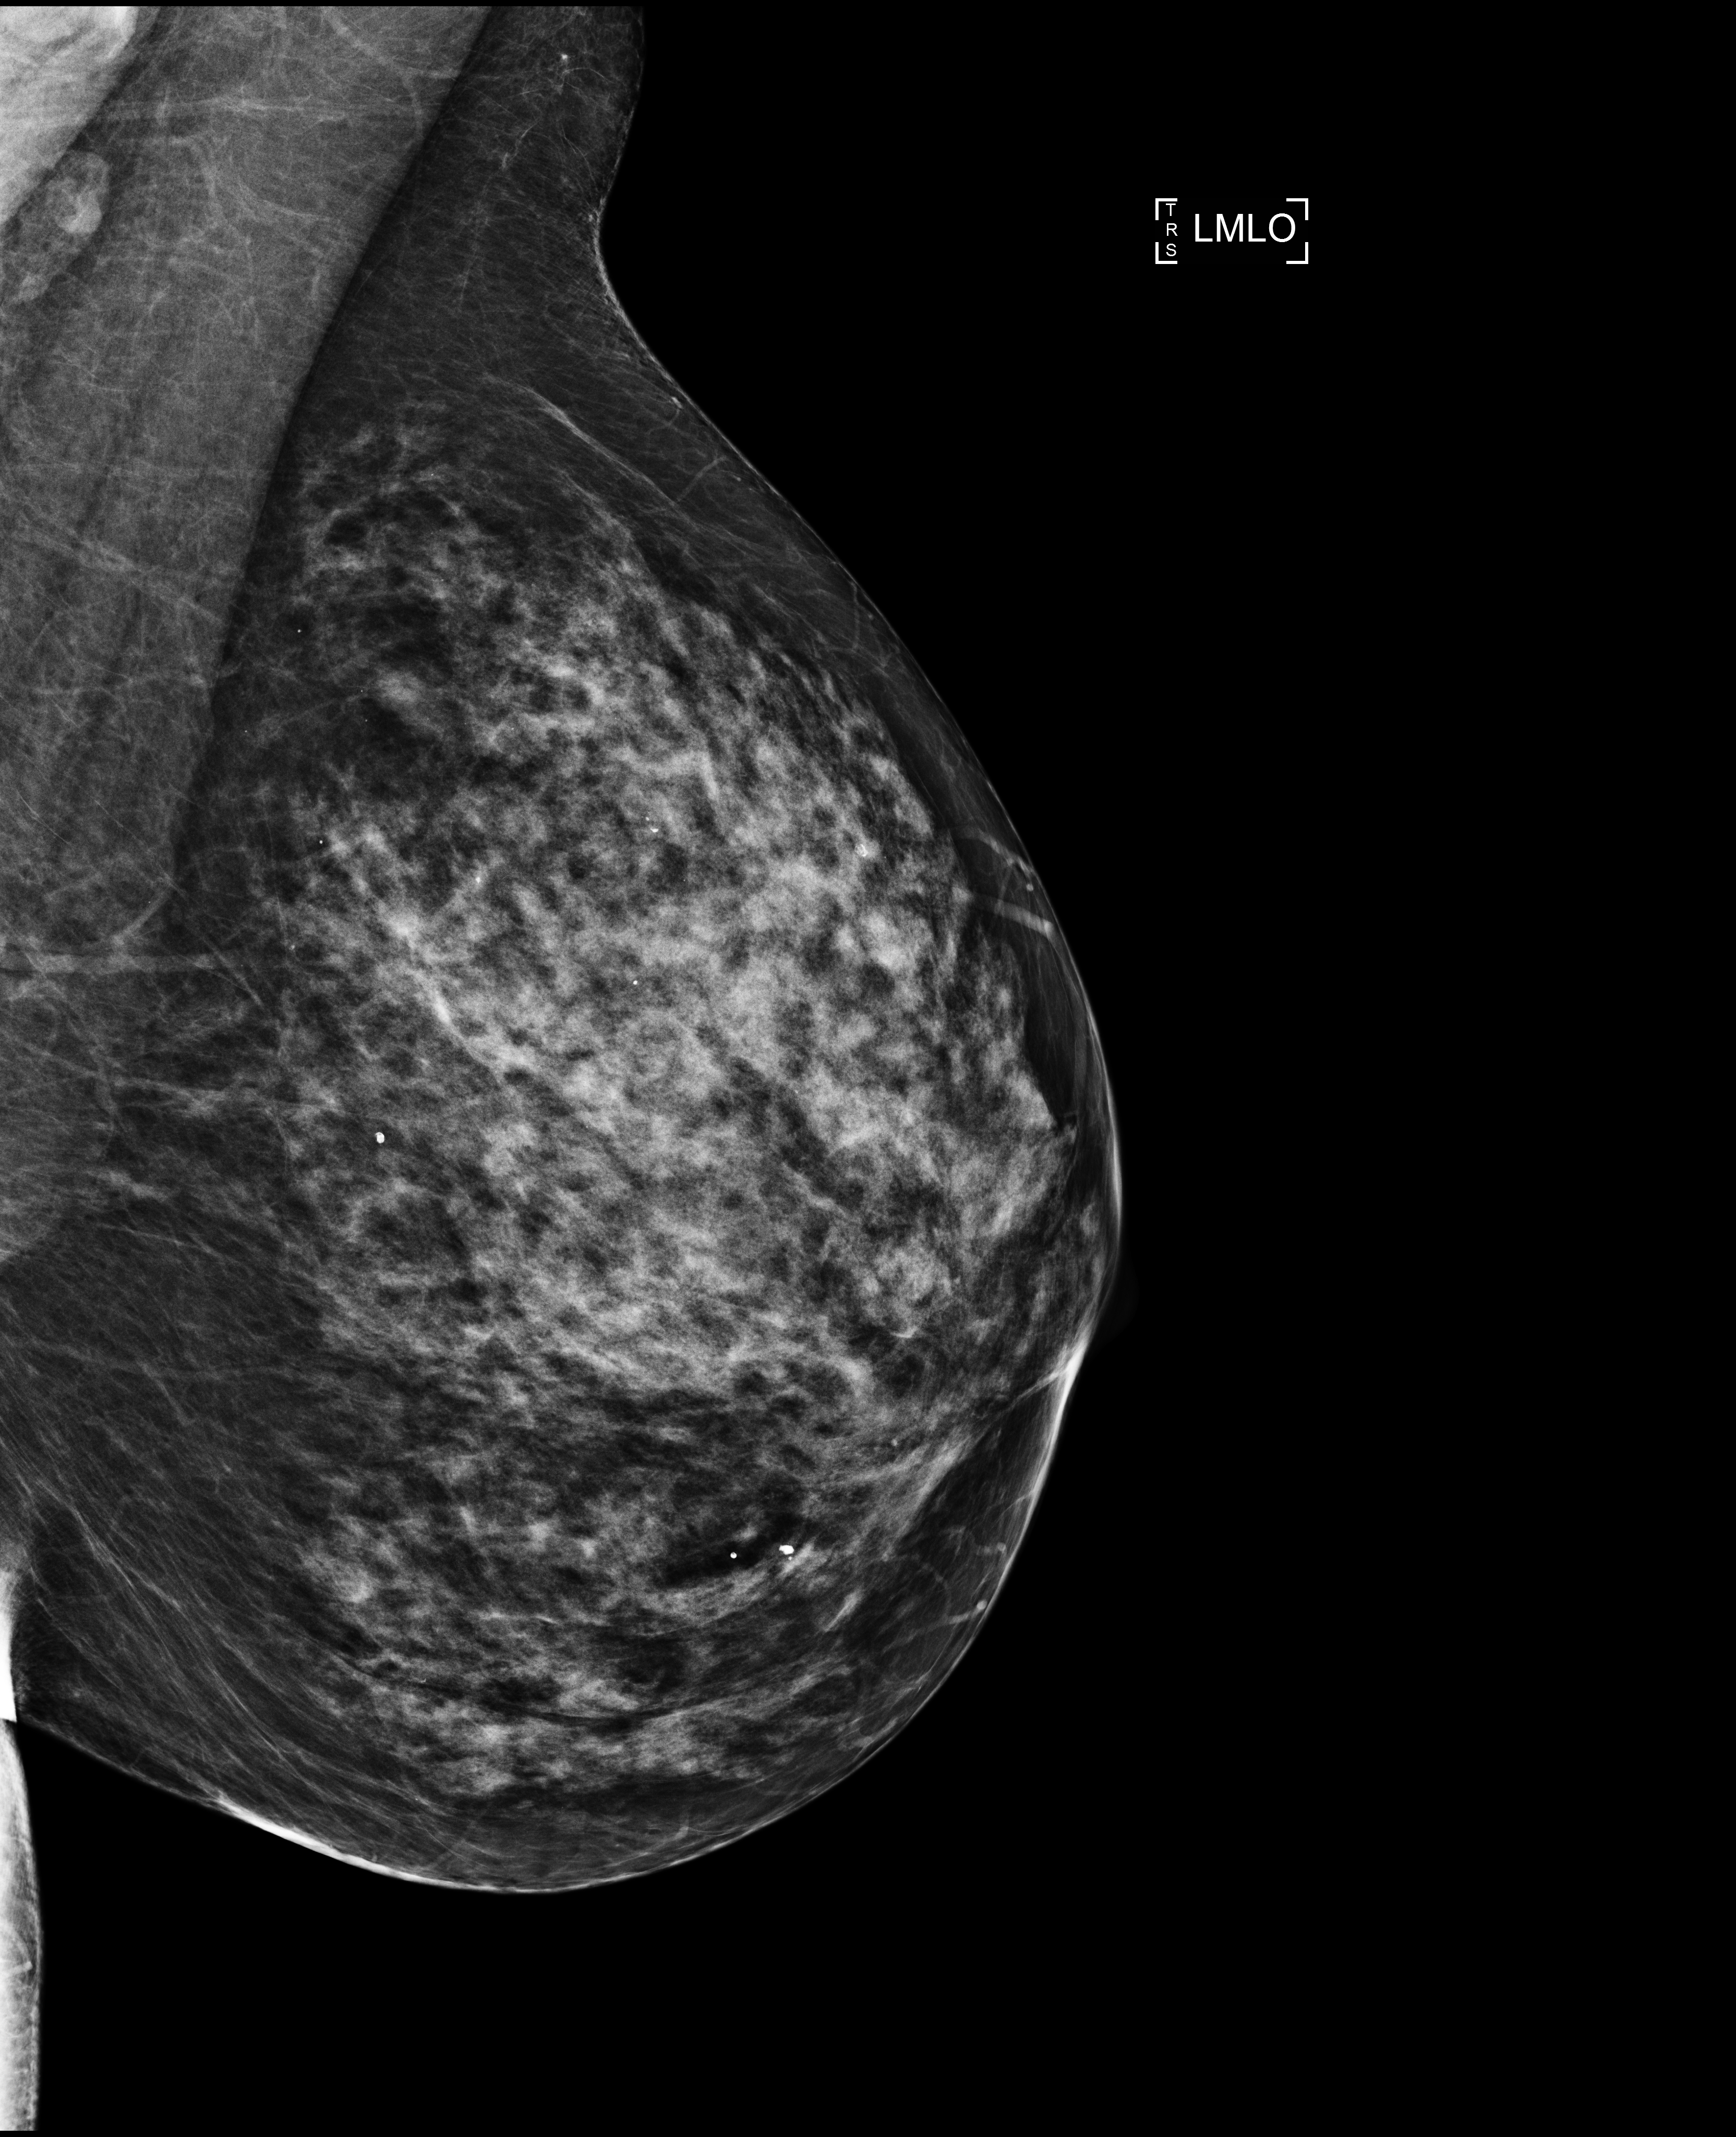
Annual screening mammography examination, compressed breast thickness 60 mm, system: Selenia Dimensions. Patient aged 63 years (female).
Image type: full-field digital mammogram. Breast: left. Projection: medio-lateral oblique projection.